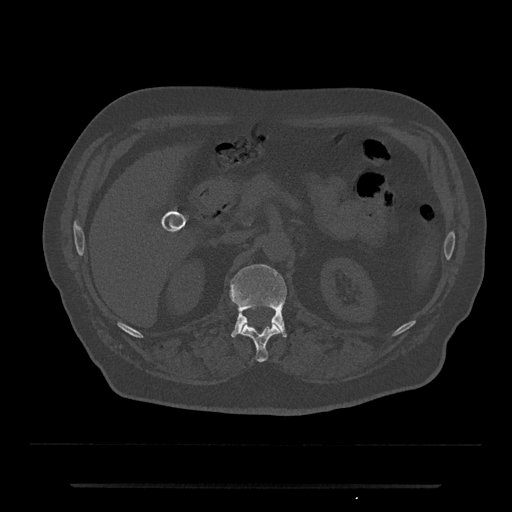
CT including the spine, one axial slice; position 561 of 797 along the scan axis; reconstruction kernel Br40s/3; bone window (W 1800 / L 400 HU); 0.5 mm slice thickness; 512 × 512 image matrix, field of view 434 × 434 mm. Patient: male, 80 years. From the clinical record (not read from this slice): primary cancer: prostate; vertebrae with lytic lesions (as recorded): L1, T11.
Structures marked on this image (semi-automatically segmented with operator editing):
- L1 vertebra: box from (x=230, y=264) to (x=287, y=338) px
- T12 vertebra: (x=242, y=324)–(x=280, y=362)